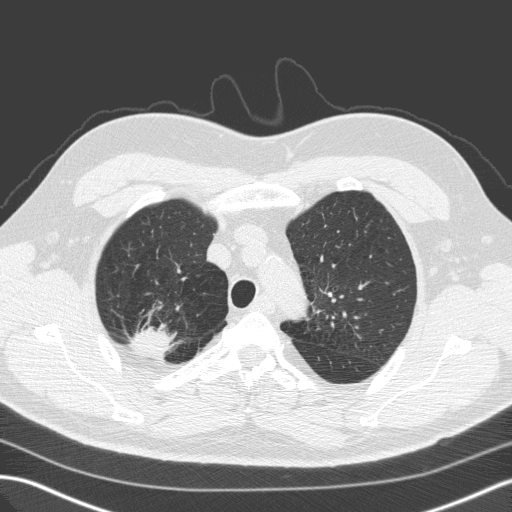
Low-dose screening chest CT, axial slice. Baseline screening round. Lung window (W 1500 / L -600 HU). Male participant, aged 59 years at enrolment.
Lesion marked by an expert reader, box from (x=118, y=313) to (x=180, y=367) px. Reader record for this screening exam (exam-level; its link to the box is not recorded): non-calcified nodule or mass ≥4 mm, right upper lobe, 28 × 25 mm, spiculated (stellate) margins, soft tissue attenuation. Official screen result: positive, change unspecified: nodule(s) >= 4 mm or enlarging nodule(s), mass(es), or other non-specific abnormalities suspicious for lung cancer. Later outcome: lung cancer diagnosed 64 days after this screen — large cell carcinoma, NOS, right upper lobe, undifferentiated (G4), stage IA (AJCC 6th edition), 25 mm at pathology.